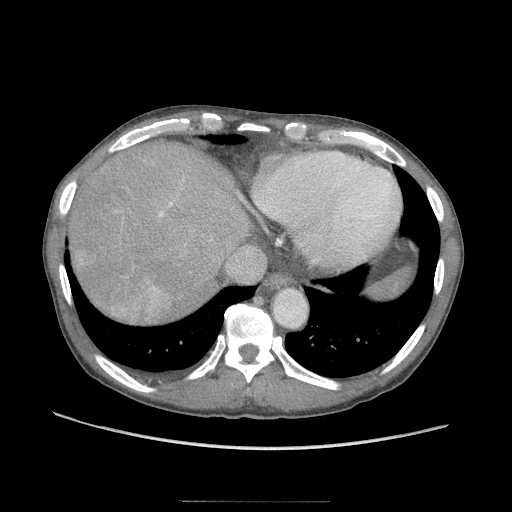
Contrast-enhanced abdominal CT (liver protocol), one axial slice; position 85 of 103 along the scan axis; soft-tissue window (W 400 / L 40 HU); 2.5 mm slice thickness; 512 × 512 image matrix, field of view 380 × 380 mm. Case-level facts recorded for this patient, not image findings: diagnosis: hepatocellular carcinoma (patient treated with transarterial chemoembolisation; whether this scan precedes or follows treatment is not stated here); TNM stage (as recorded): Stage-IIIA; Child-Pugh class: A.
Outlined on this slice (semi-automatically segmented with operator editing):
- abdominal aorta: box from (x=274, y=290) to (x=306, y=326) px
- liver parenchyma outside the tumour (the mass and vessels are separate outlines, so this box may not span the whole liver): (x=70, y=138)–(x=245, y=314)
- mass: (x=113, y=296)–(x=129, y=313)
- liver vessels: (x=133, y=287)–(x=157, y=303)